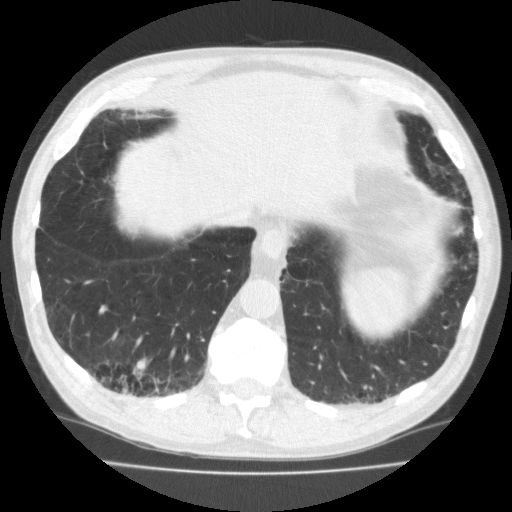
Low-dose screening chest CT, one axial slice. Position 53 of 195 along the scan axis. Reconstruction kernel FC10. 120 kVp. Lung window (W 1500 / L -600 HU). 512 × 512 image matrix.
Annotated regions visible in this slice (manually delineated by an expert):
- lesion 1 (tumor, lower lobe of right lung): box from (x=133, y=358) to (x=148, y=380) px